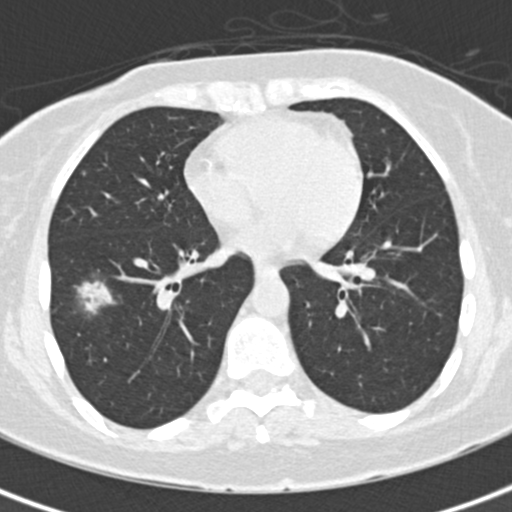
Low-dose screening chest CT, one axial slice. Slice 74 of 171 in the series (ordered by position). 120 kVp. Lung window (W 1500 / L -600 HU). 2 mm slice thickness. 512 × 512 image matrix, field of view 284 × 284 mm.
Outlined on this slice (outlined manually by an expert reader):
- lesion 1 (tumor, lower lobe of right lung): bounding box <74,281,116,314> (left, top, right, bottom; pixels)